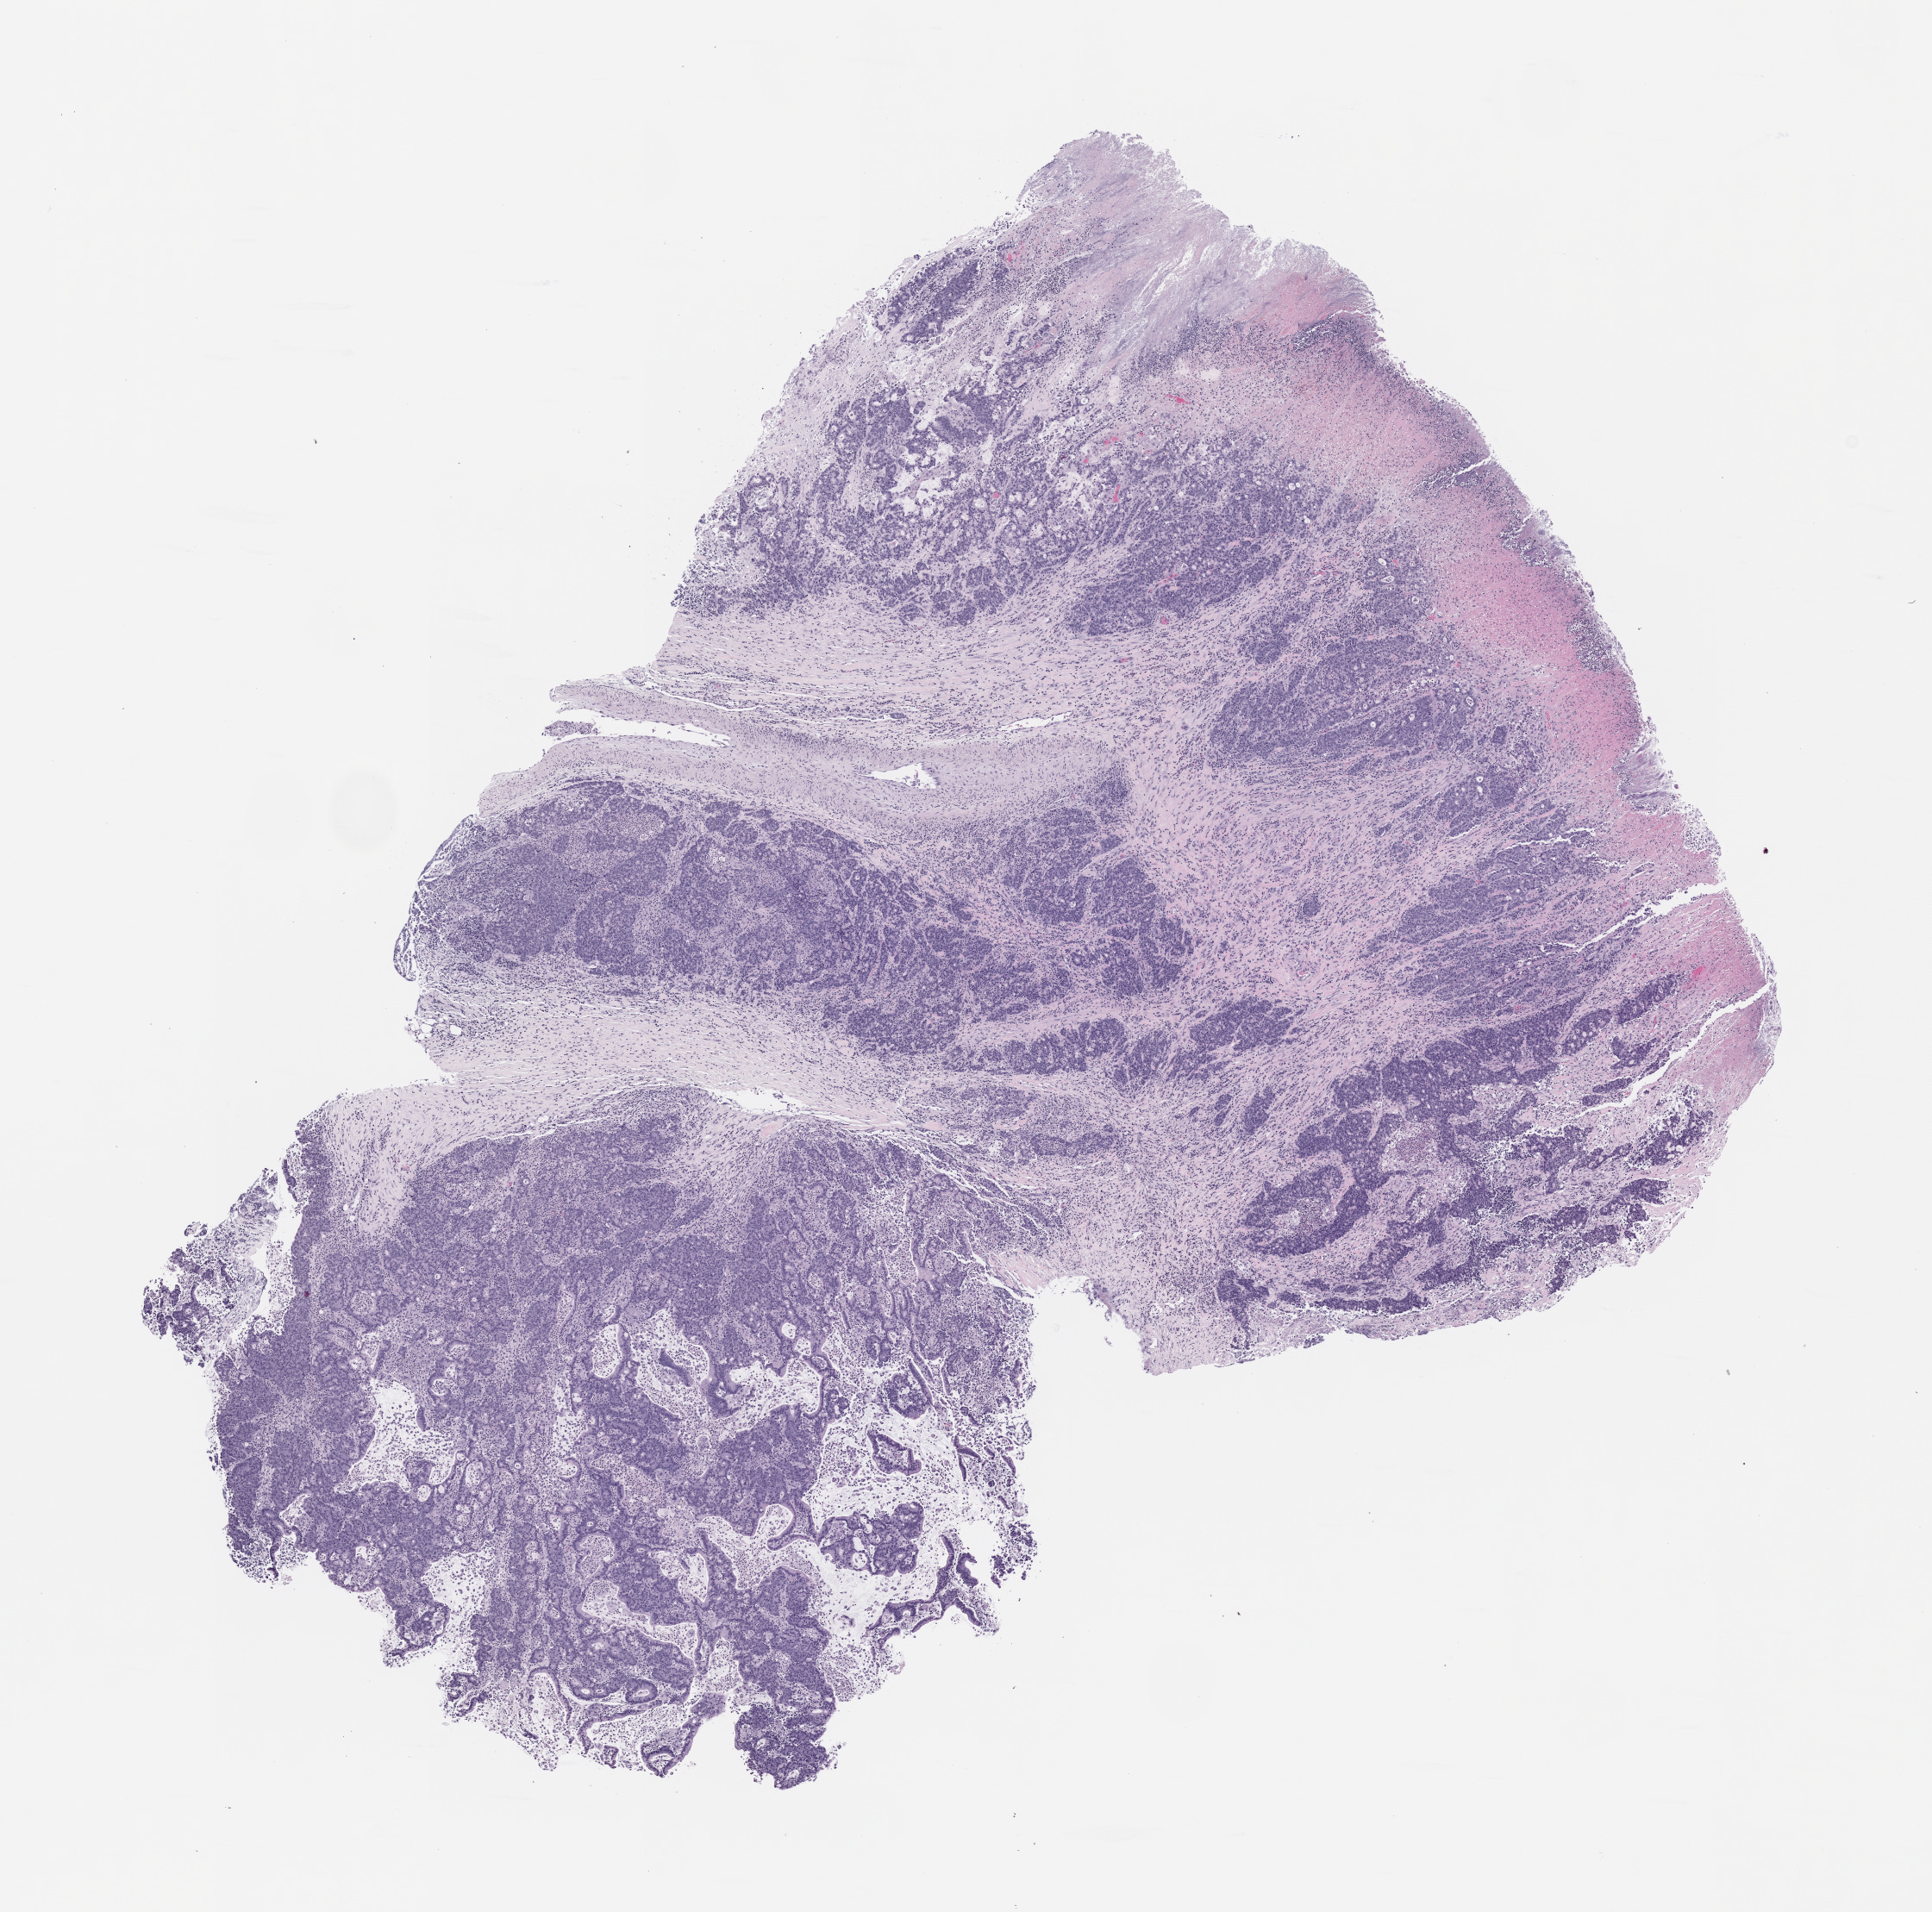
Digitized haematoxylin and eosin-stained section of the patient's (originator) tumor tissue — a low-resolution overview of the entire scanned area, about 9.0 x 8.9 mm. Formalin-fixed, paraffin-embedded (FFPE) tissue. Tumor site category: colon. Patient: female.
Diagnosis: Colon Adenocarcinoma.